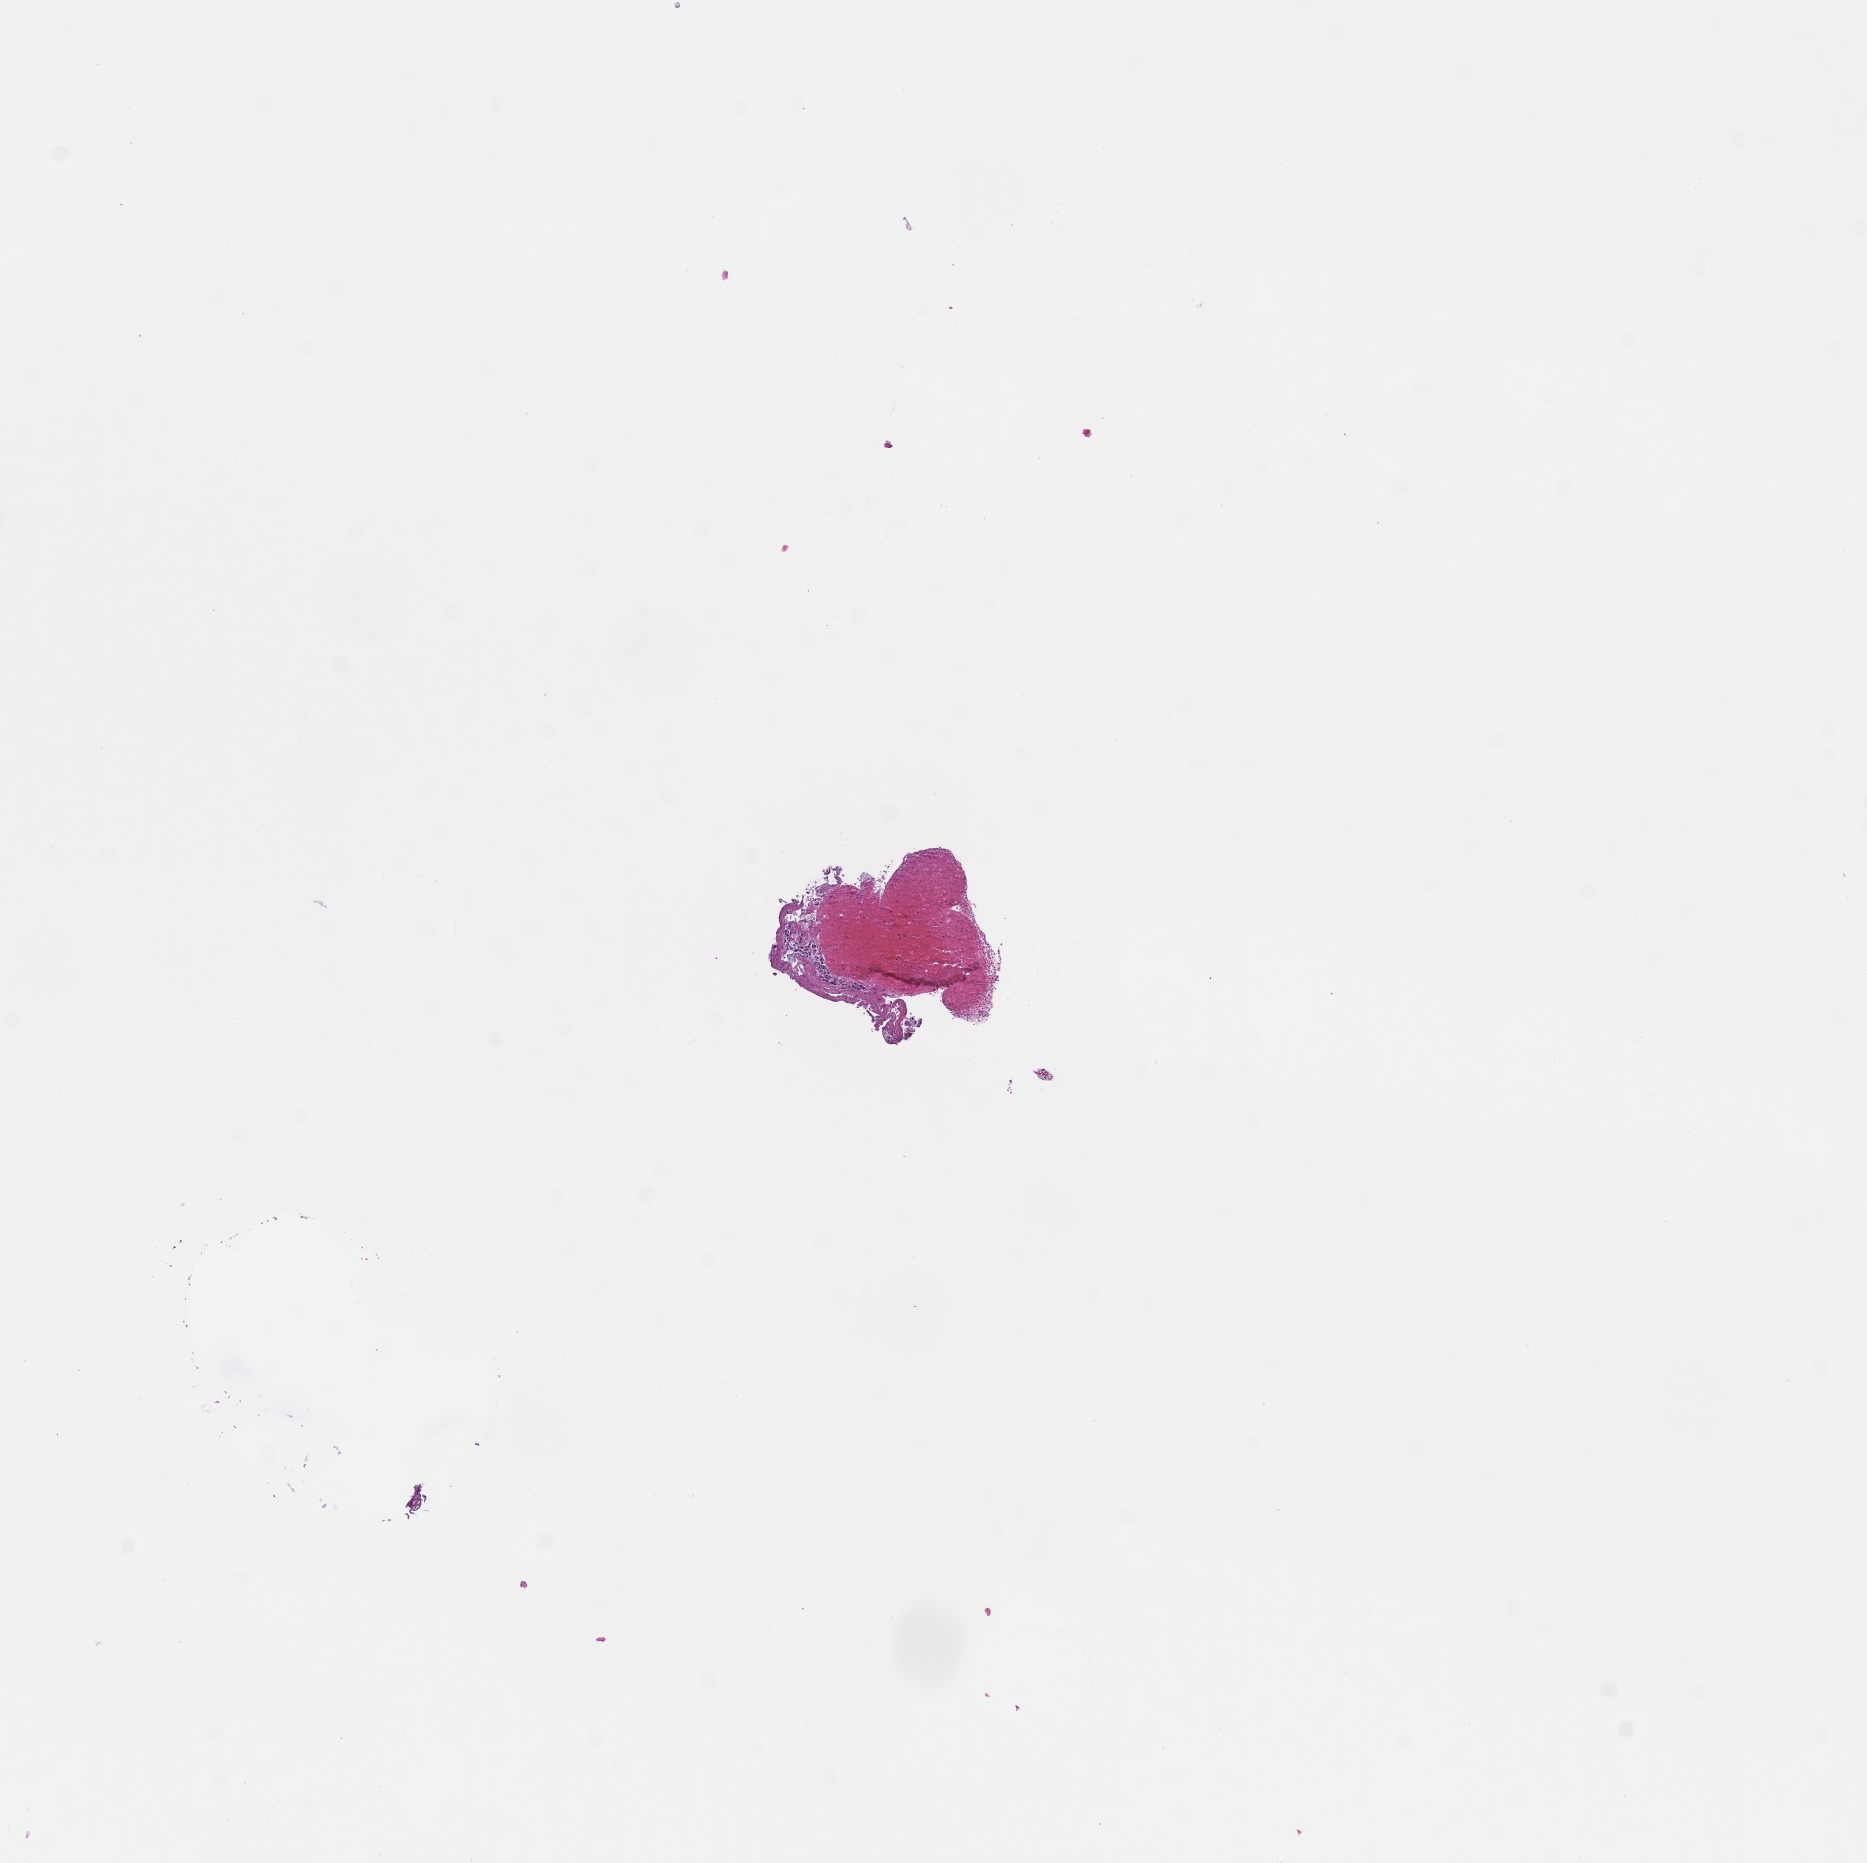
Whole-slide image, hematoxylin and eosin (H&E) stain — whole scanned area (about 7.5 x 7.5 mm) shown as a low-resolution overview. FFPE section. Site: lung. Specimen time point: collected at disease progression. Patient: female.
• this section: primary tumor
• diagnosis: Non-Small Cell Lung Carcinoma